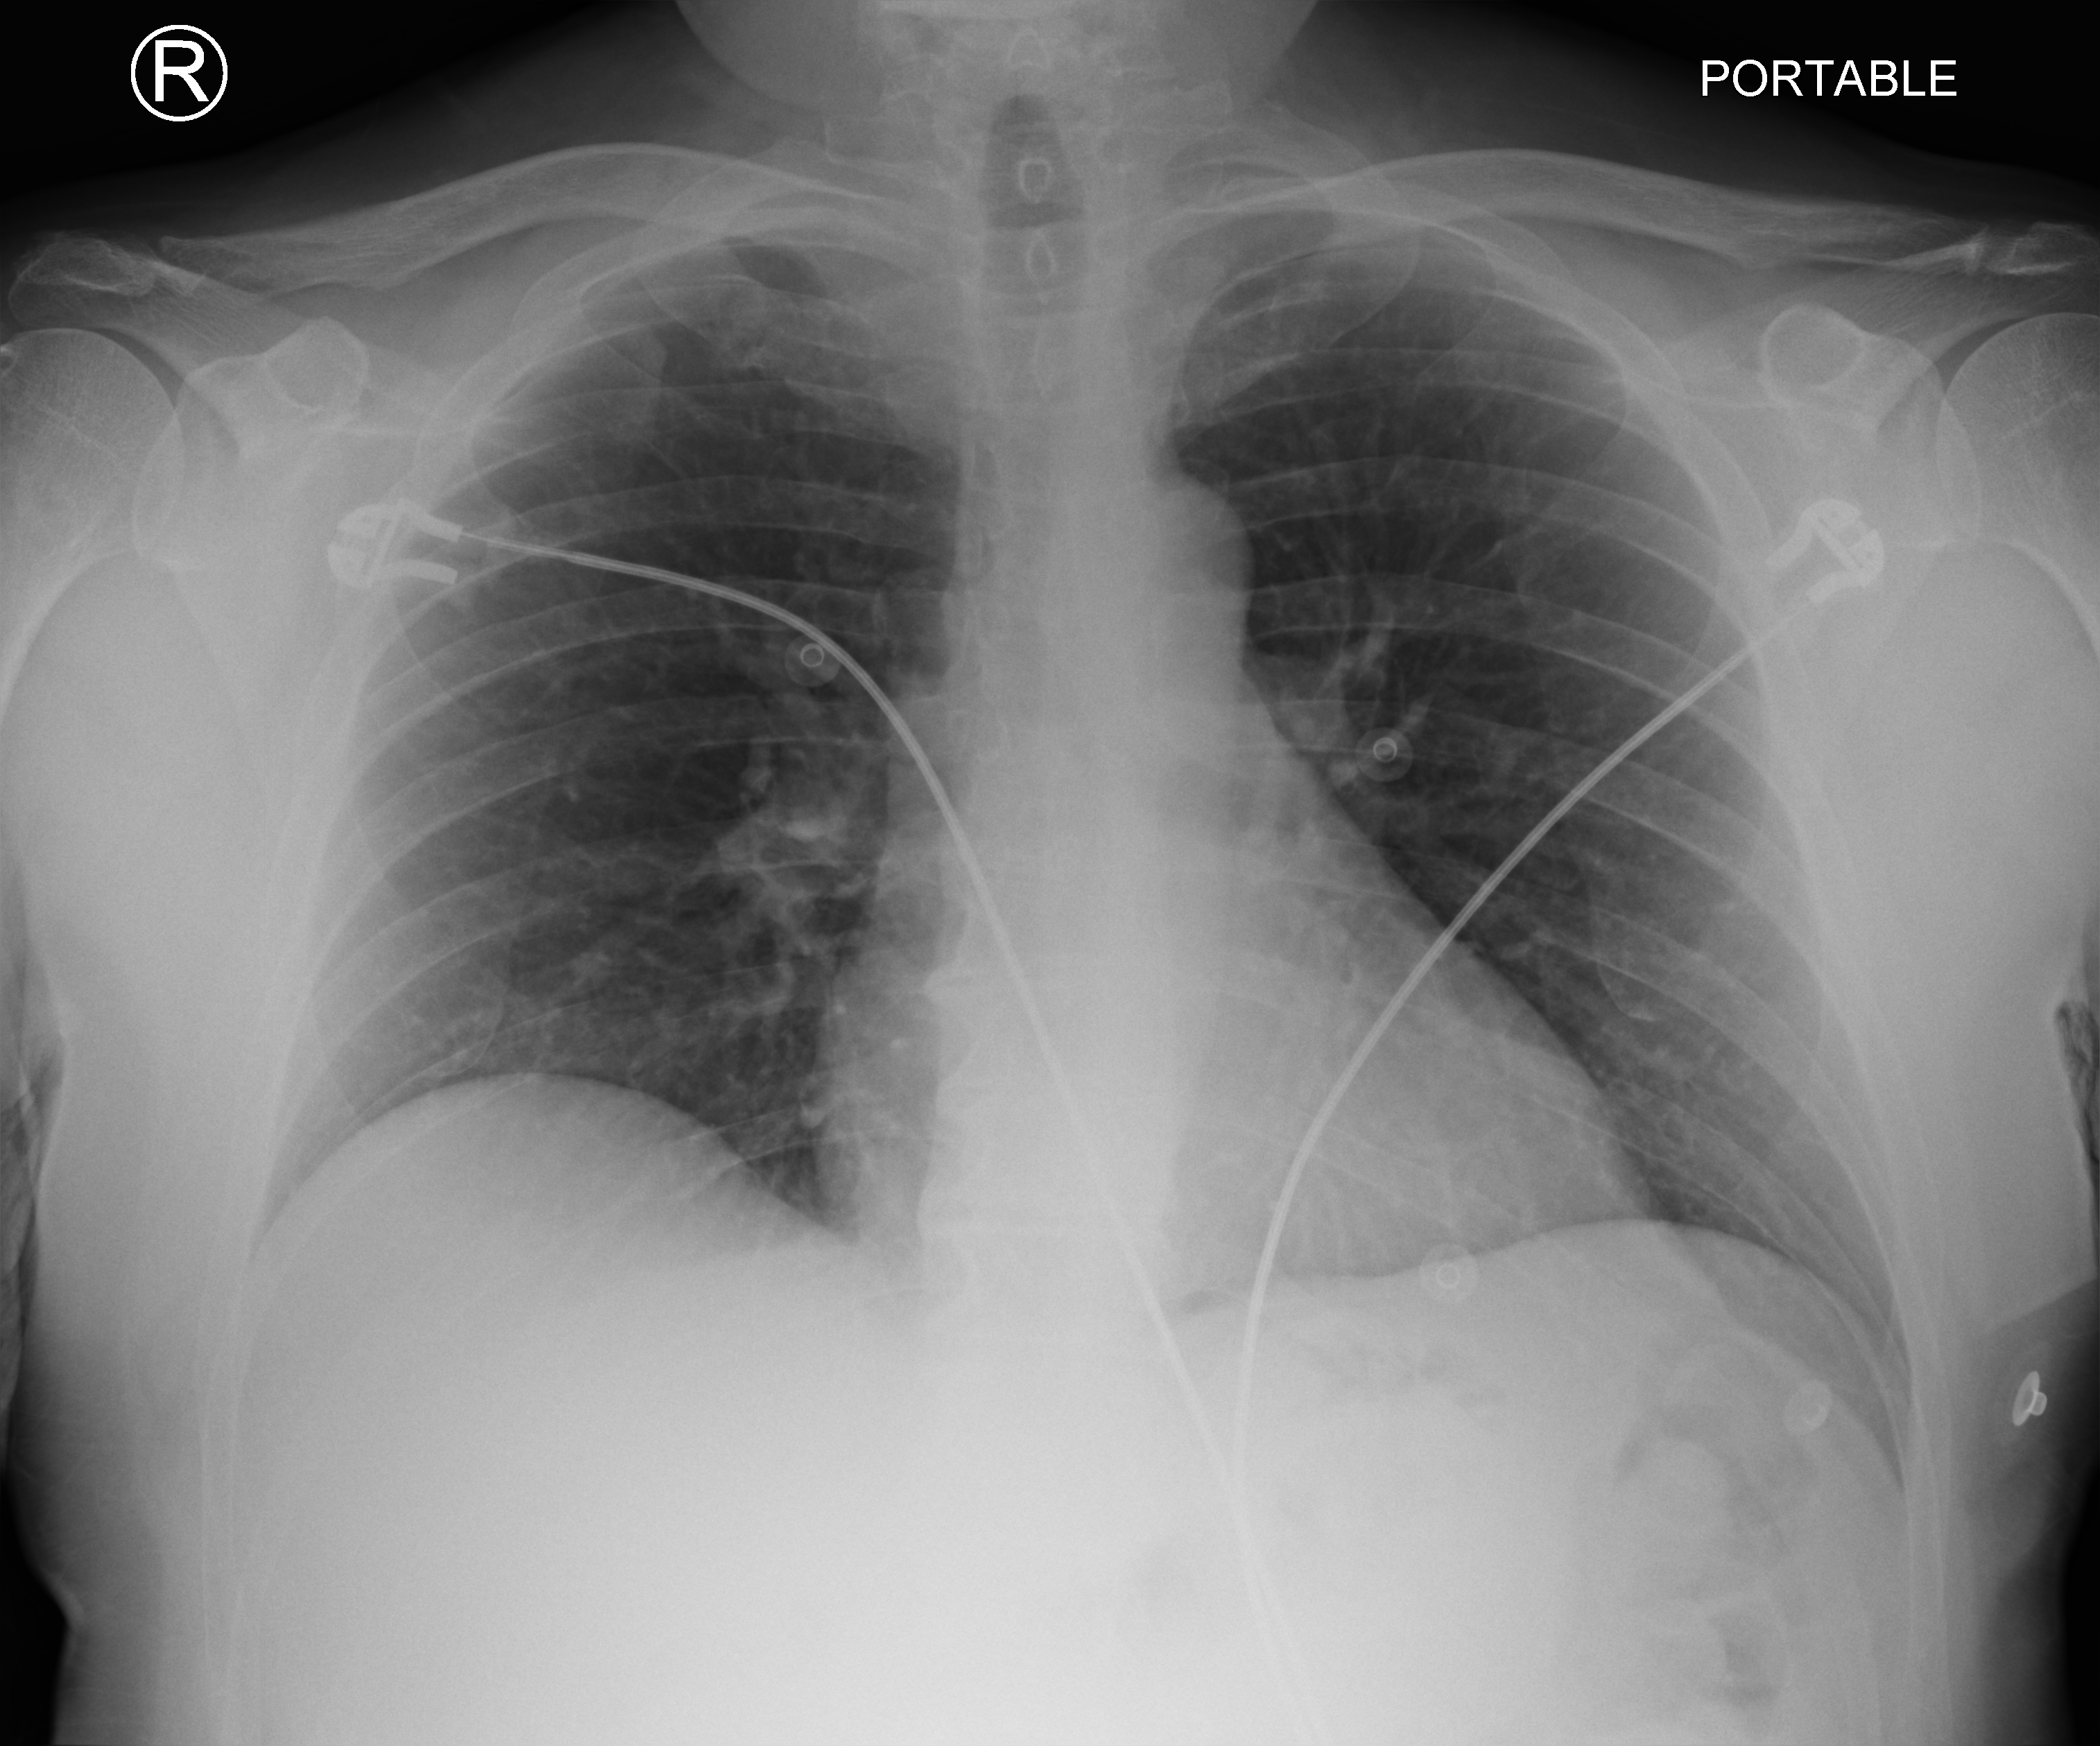
Chest X-ray (portable), anteroposterior (AP) projection. Patient hospitalised with COVID-19; male, aged 18–59 years.
Admission-level facts for this patient (not findings on this image; timing relative to this image not recorded): mechanically ventilated during this hospital stay: no; hypertension (admission record): yes; COPD (admission record): no.